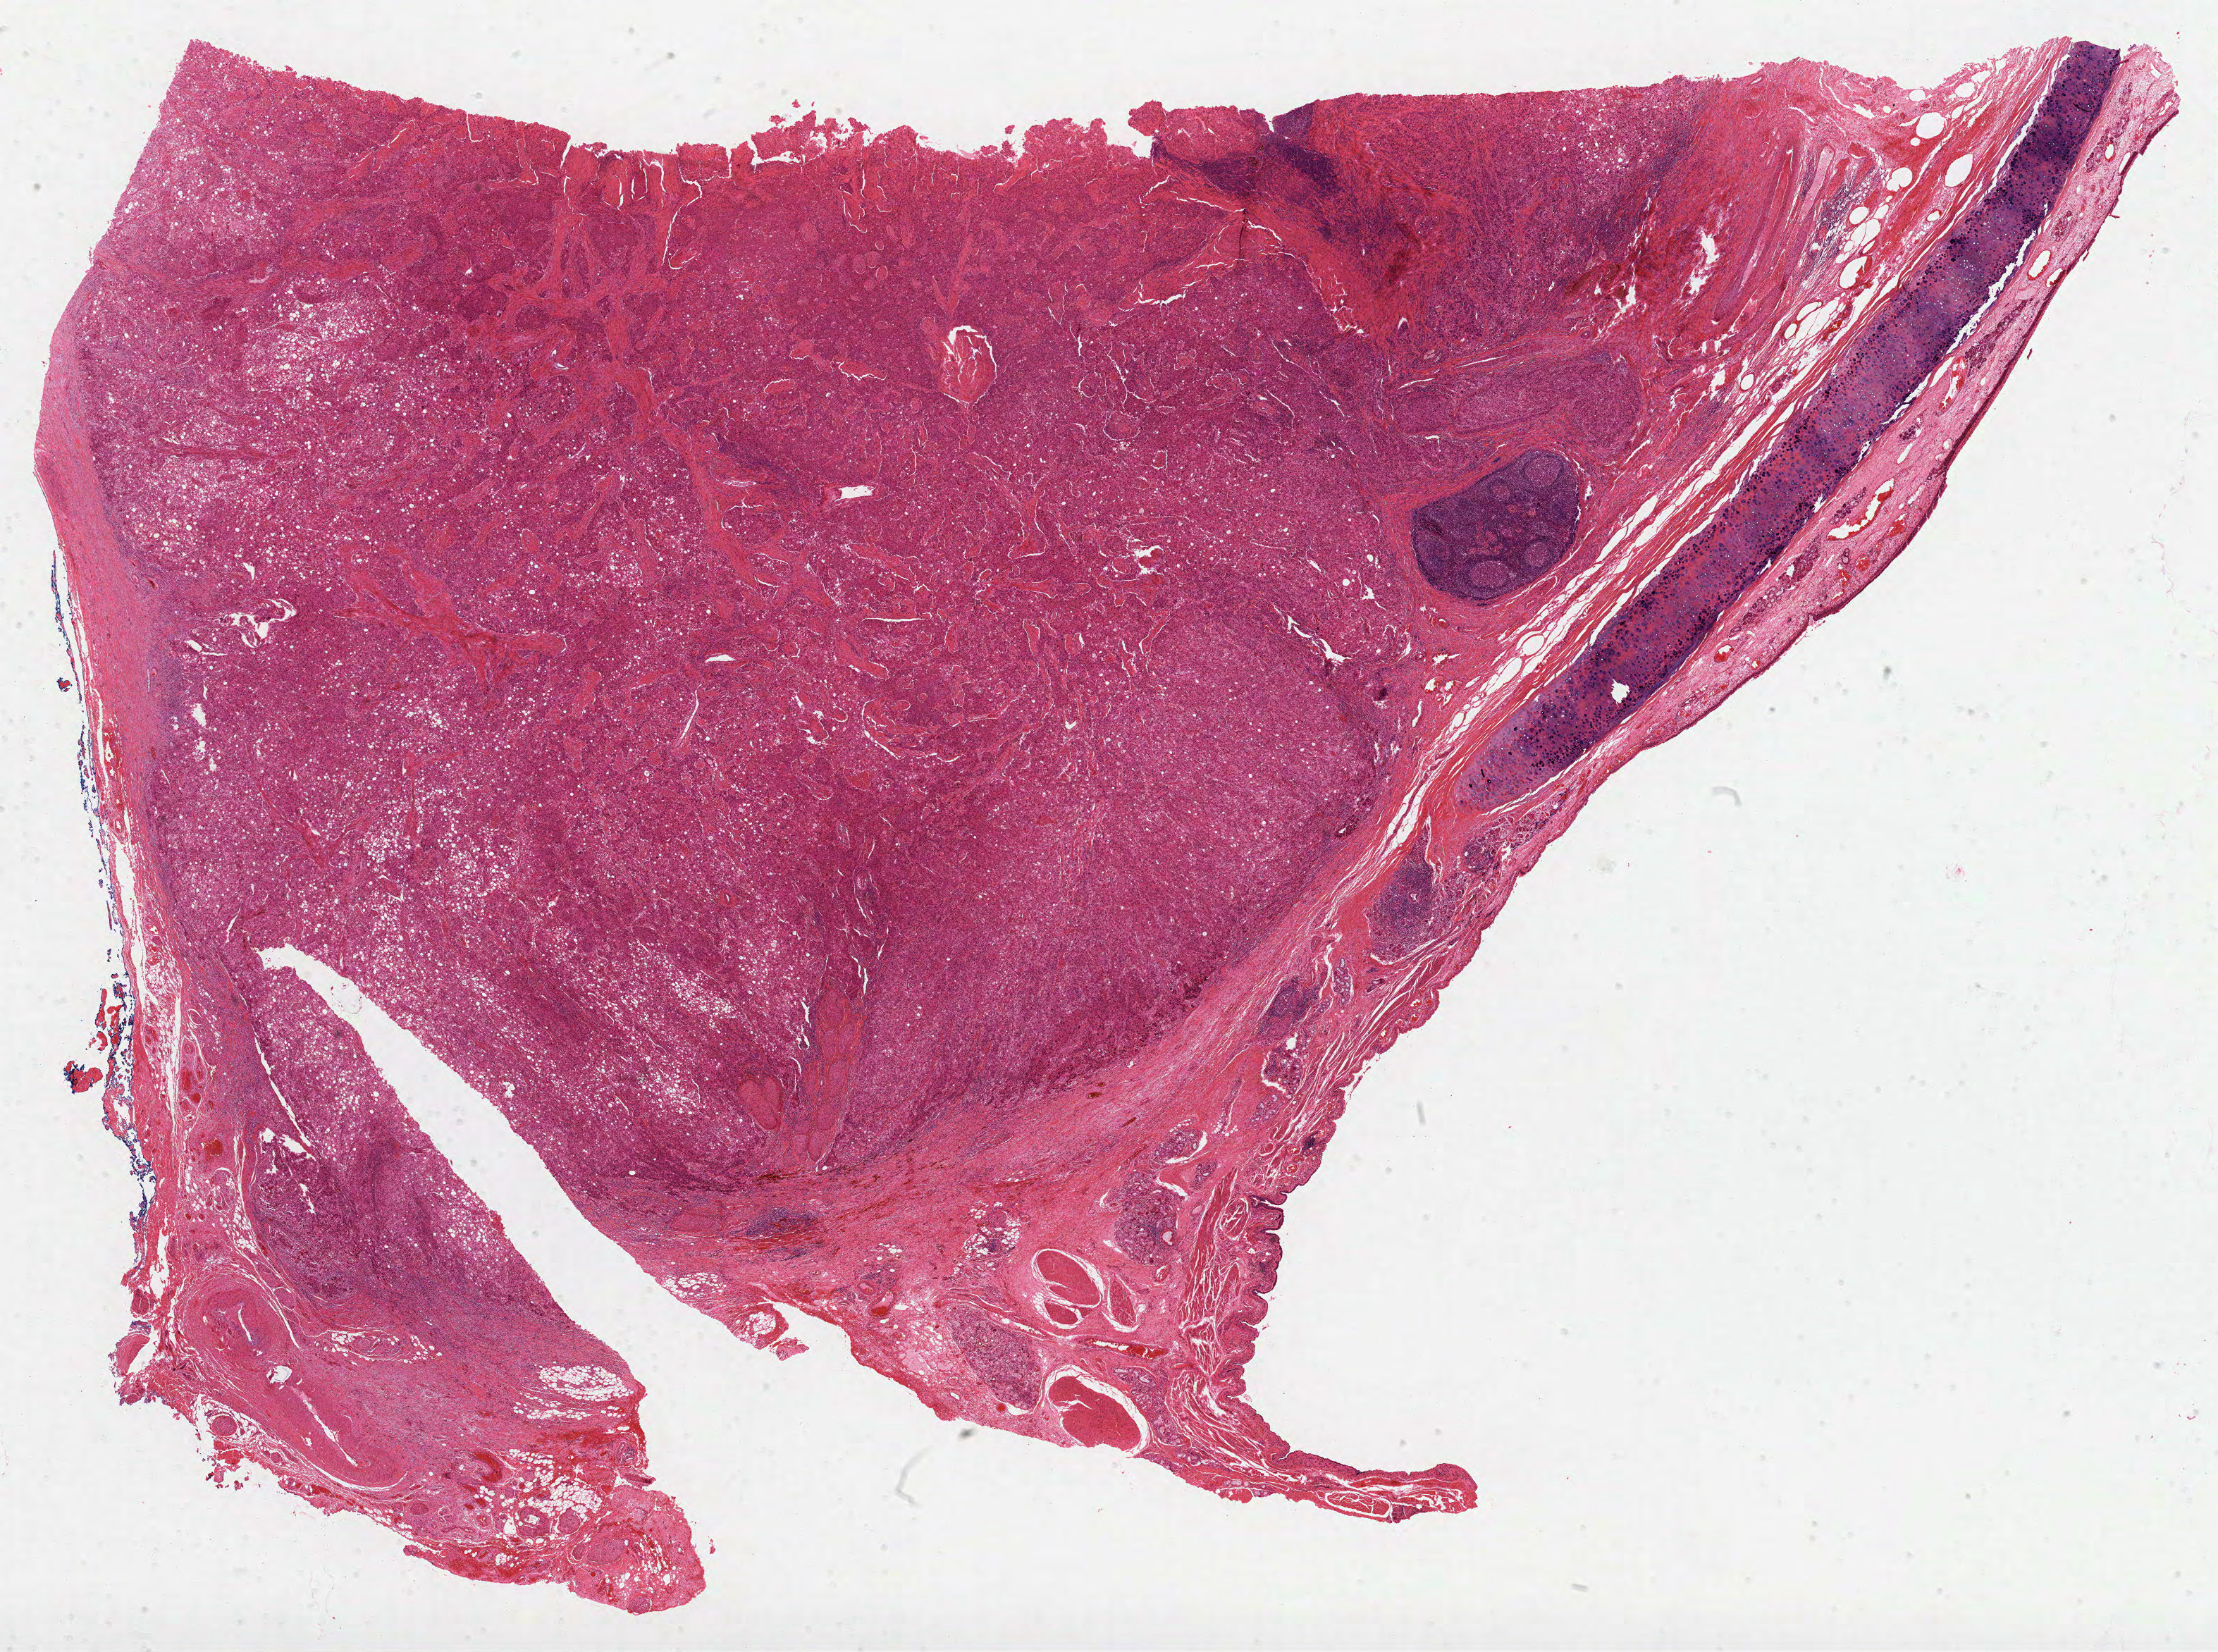
Whole-slide histology image, Hematoxylin and eosin (H&E) stained — whole scanned area (about 25.4 x 18.9 mm, acquisition: 40x scan) shown as a low-resolution overview, formalin-fixed paraffin-embedded (FFPE) diagnostic section, primary tumour sample from the lung. Female, age 74 years at initial diagnosis.
• pathologic diagnosis: Squamous cell carcinoma, keratinizing, NOS (lower lobe, lung)
• AJCC pathologic stage: IIB (7th edition)